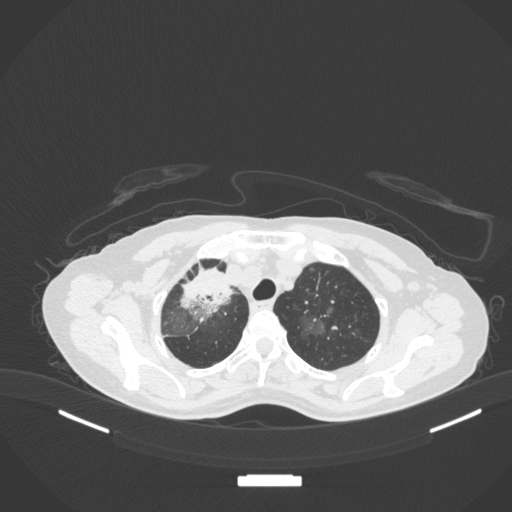
Chest CT, one axial slice; position 270 of 311 along the scan axis; lung window (W 1500 / L -600 HU); 1 mm slice thickness; 512 × 512 image matrix. Female patient, age 59 years. Case-level facts recorded for this patient, not image findings: clinical TNM (as recorded): T3 N0 M0.
Structures marked on this image (rectangle marked by the reading radiologist):
- lung tumour (recorded histology: adenocarcinoma): bounding box (x1, y1, x2, y2) in pixels: (171, 259, 234, 318)